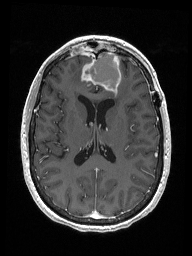
Brain MRI from a brain-tumour surgery series, one axial slice. Position 74 of 192 along the scan axis. T1-weighted post-contrast. 192 × 256 image matrix, field of view 187 × 250 mm. Case-level facts recorded for this patient, not image findings: histopathology: Metastastic Carcinoma from Breast primary; tumour location: Right Frontal.
Structures marked on this image (outlined manually by an expert reader):
- previous resection cavity: box from (x=86, y=53) to (x=122, y=90) px